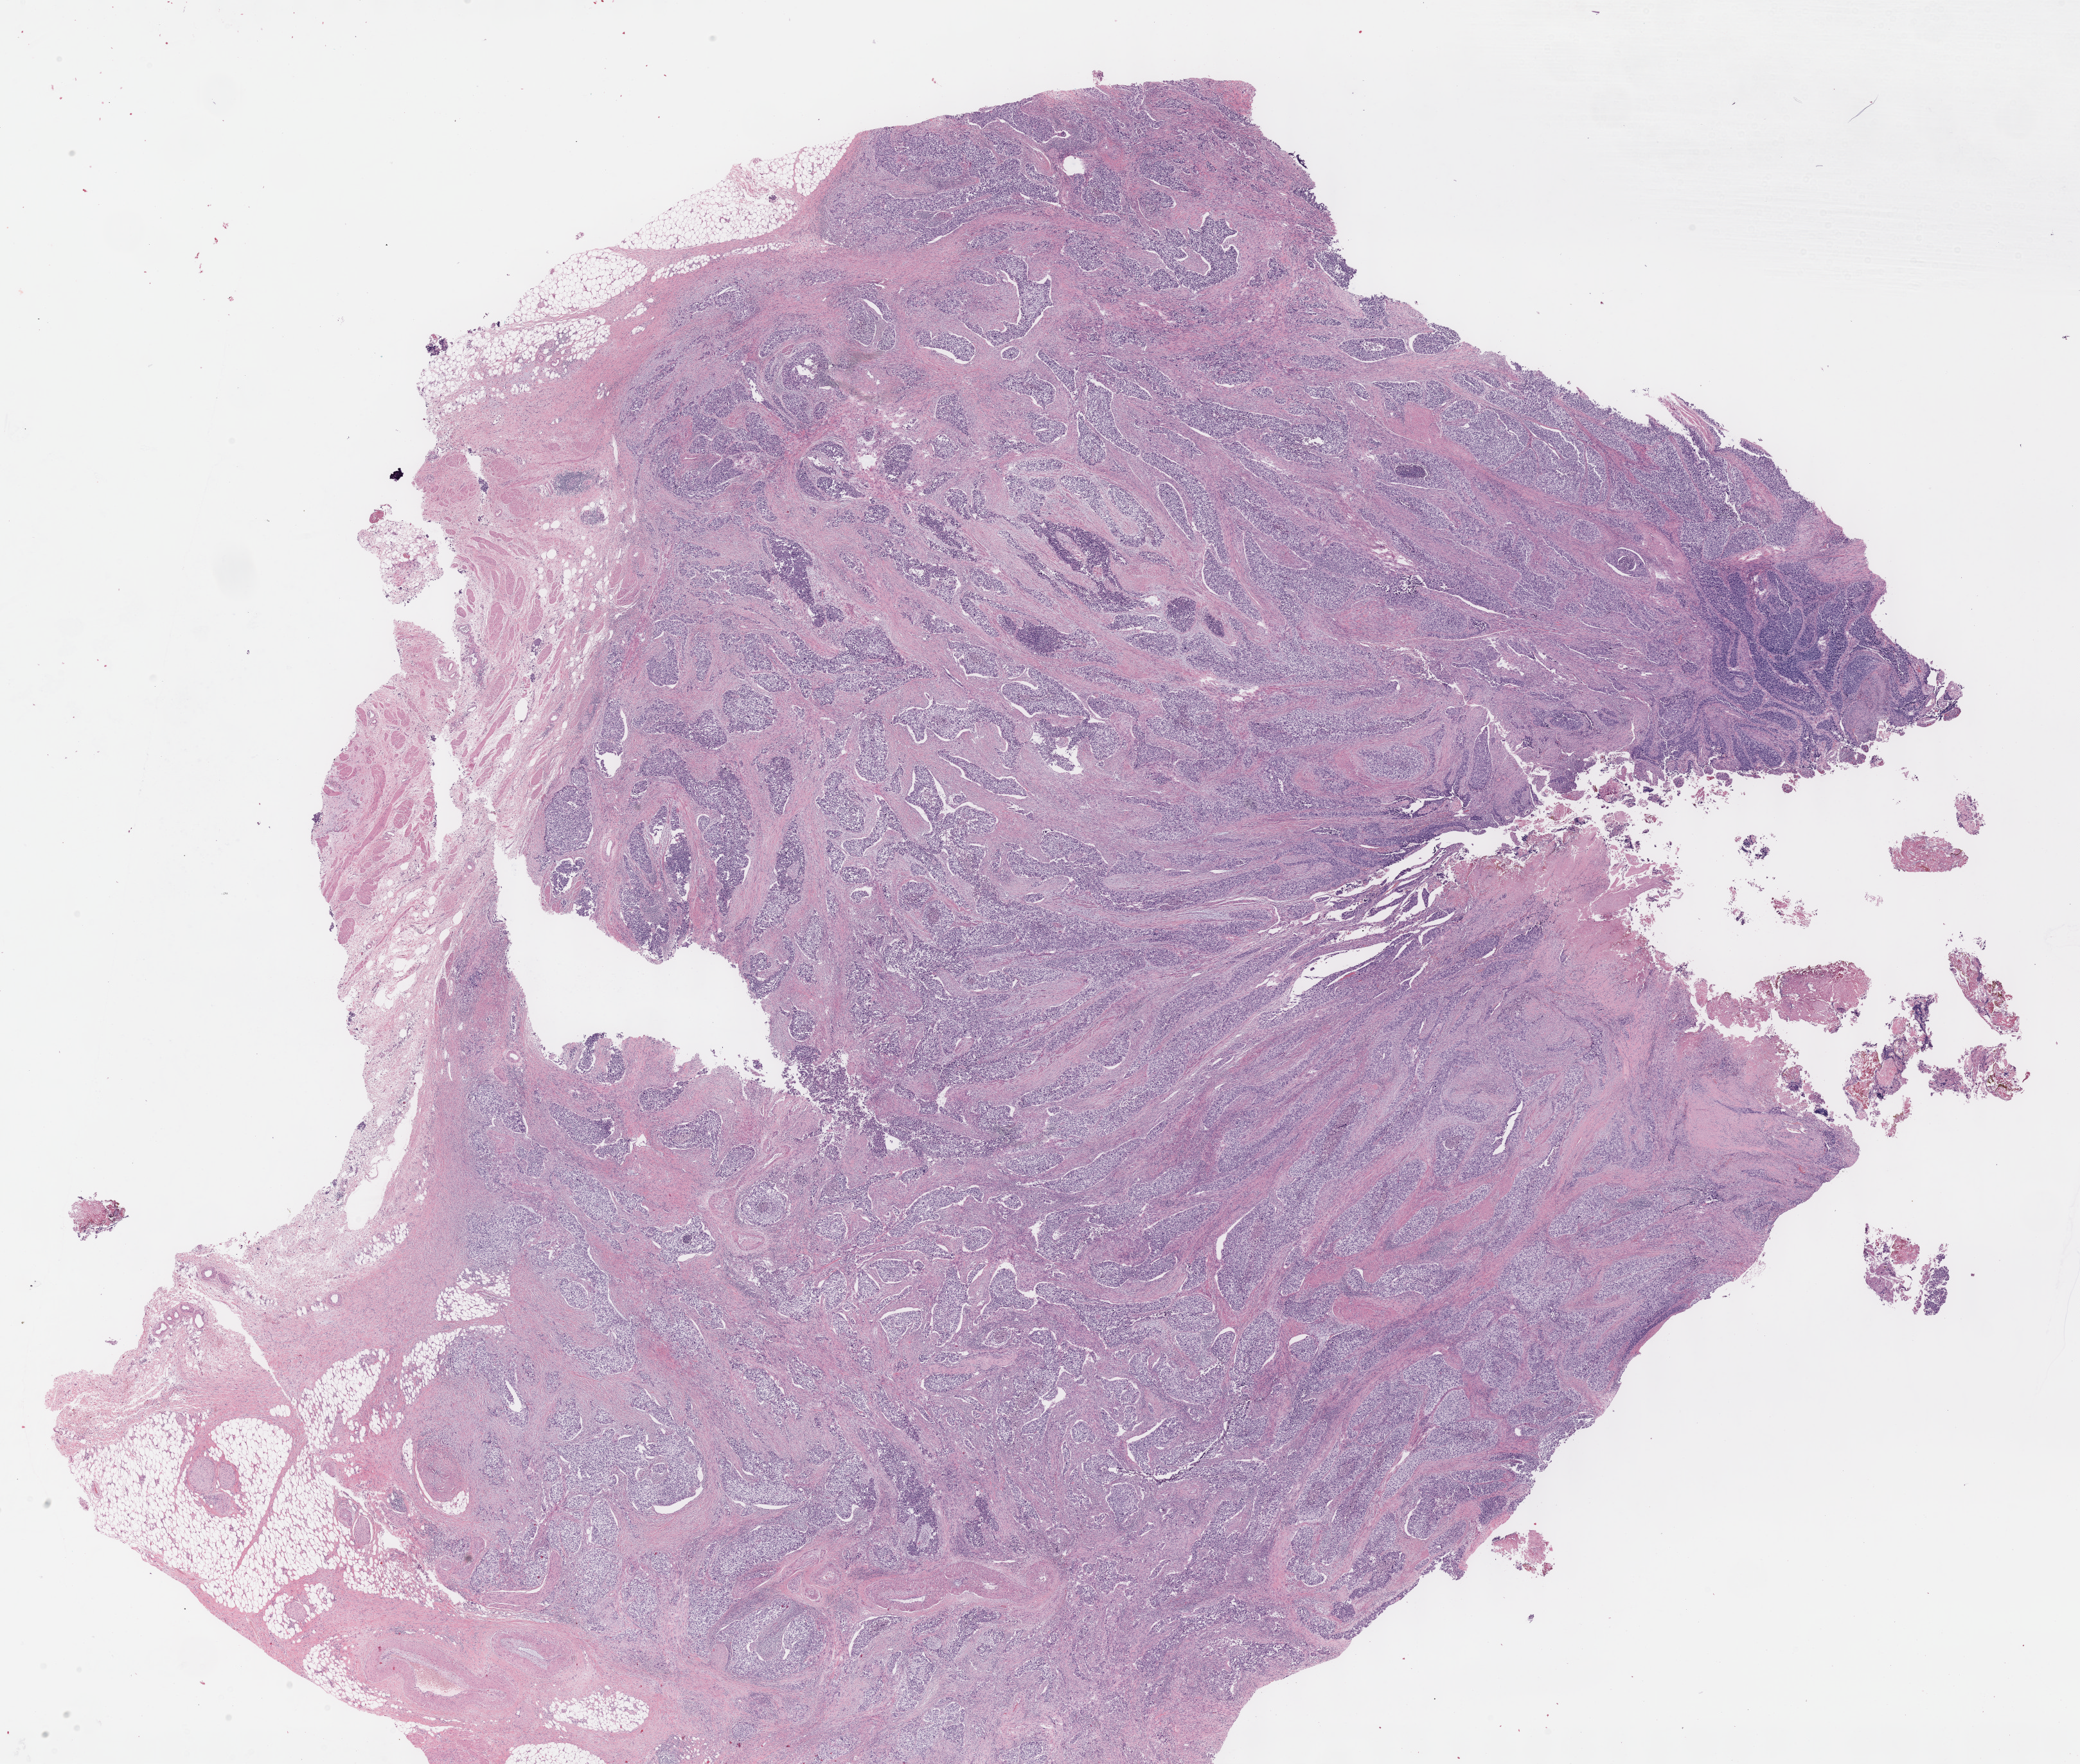
Digitized H&E tissue section (whole slide) — a low-resolution overview of the entire scanned area, about 26.2 x 22.2 mm; formalin-fixed paraffin-embedded (FFPE) diagnostic section; primary tumour sample from the bladder. Male, age 65 years at initial diagnosis. Histologic grade: high grade.
• AJCC pathologic stage: III (7th edition)
• histologic diagnosis: Transitional cell carcinoma (lateral wall of bladder)